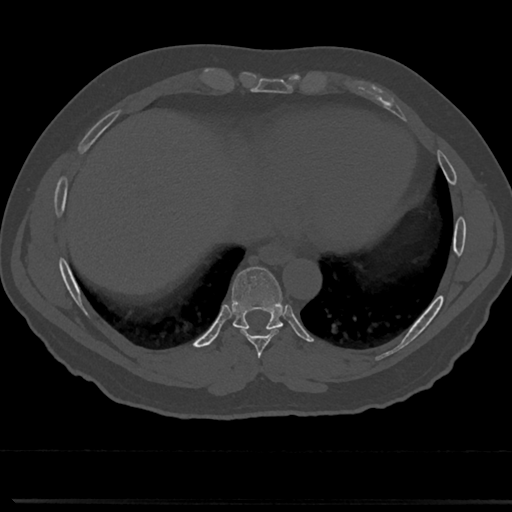
CT including the spine, one axial slice. Slice 329 of 817 in the series (ordered by position). 120 kVp. Bone window (W 1800 / L 400 HU). 0.5 mm slice thickness. 512 × 512 image matrix. Patient: male, 61 years. From the clinical record (not read from this slice): primary cancer: prostate.
Outlined on this slice (semi-automatic segmentation, software-assisted and operator-edited):
- T7 vertebra: bounding box [x1, y1, x2, y2] px = [258, 349, 266, 376]
- T8 vertebra: [211, 270, 310, 357]